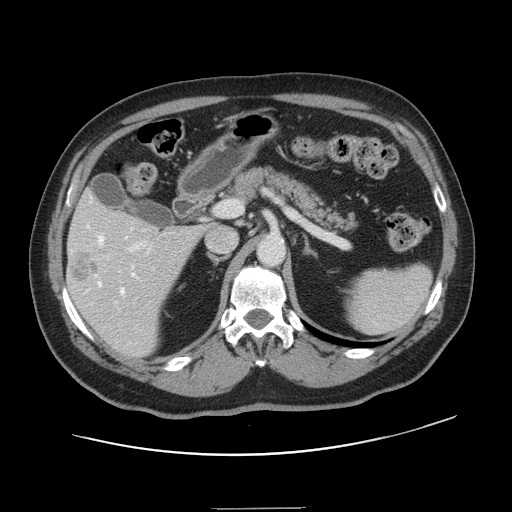
Contrast-enhanced abdominal CT, one axial slice; 120 kVp; intravenous contrast given; soft-tissue window (W 400 / L 40 HU); 2.5 mm slice thickness; 512 × 512 image matrix. Male patient, age 62 years. From the clinical record (not read from this slice): diagnosis: colorectal cancer liver metastases, imaged before liver resection; multiple liver metastases: yes; largest metastasis: 2.7 cm; disease in both lobes: no.
Structures marked on this image (manually delineated by an expert):
- hepatic veins: bounding box [x1, y1, x2, y2] px = [88, 197, 136, 295]
- liver: [67, 194, 204, 357]
- planned liver remnant (the part of the liver to remain after resection): [71, 194, 139, 234]
- portal vein (with intrahepatic branches): [115, 206, 220, 303]
- liver metastasis: [73, 254, 99, 283]